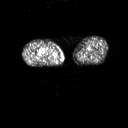
FDG PET of an extremity soft-tissue mass (from a PET/CT study), one axial slice. Position 230 of 311 along the scan axis. 3.27 mm slice thickness. 128 × 128 image matrix. Patient: male, 50 years. From the clinical record (not read from this slice): histological type: undifferentiated - pleiomorphic; grade: high; site of the primary tumour: right thigh.
Structures marked on this image (expert contour drawn on MRI and transferred to this co-registered scan by the dataset authors):
- gross tumour volume including surrounding oedema: bounding box [x1, y1, x2, y2] px = [45, 54, 47, 56]